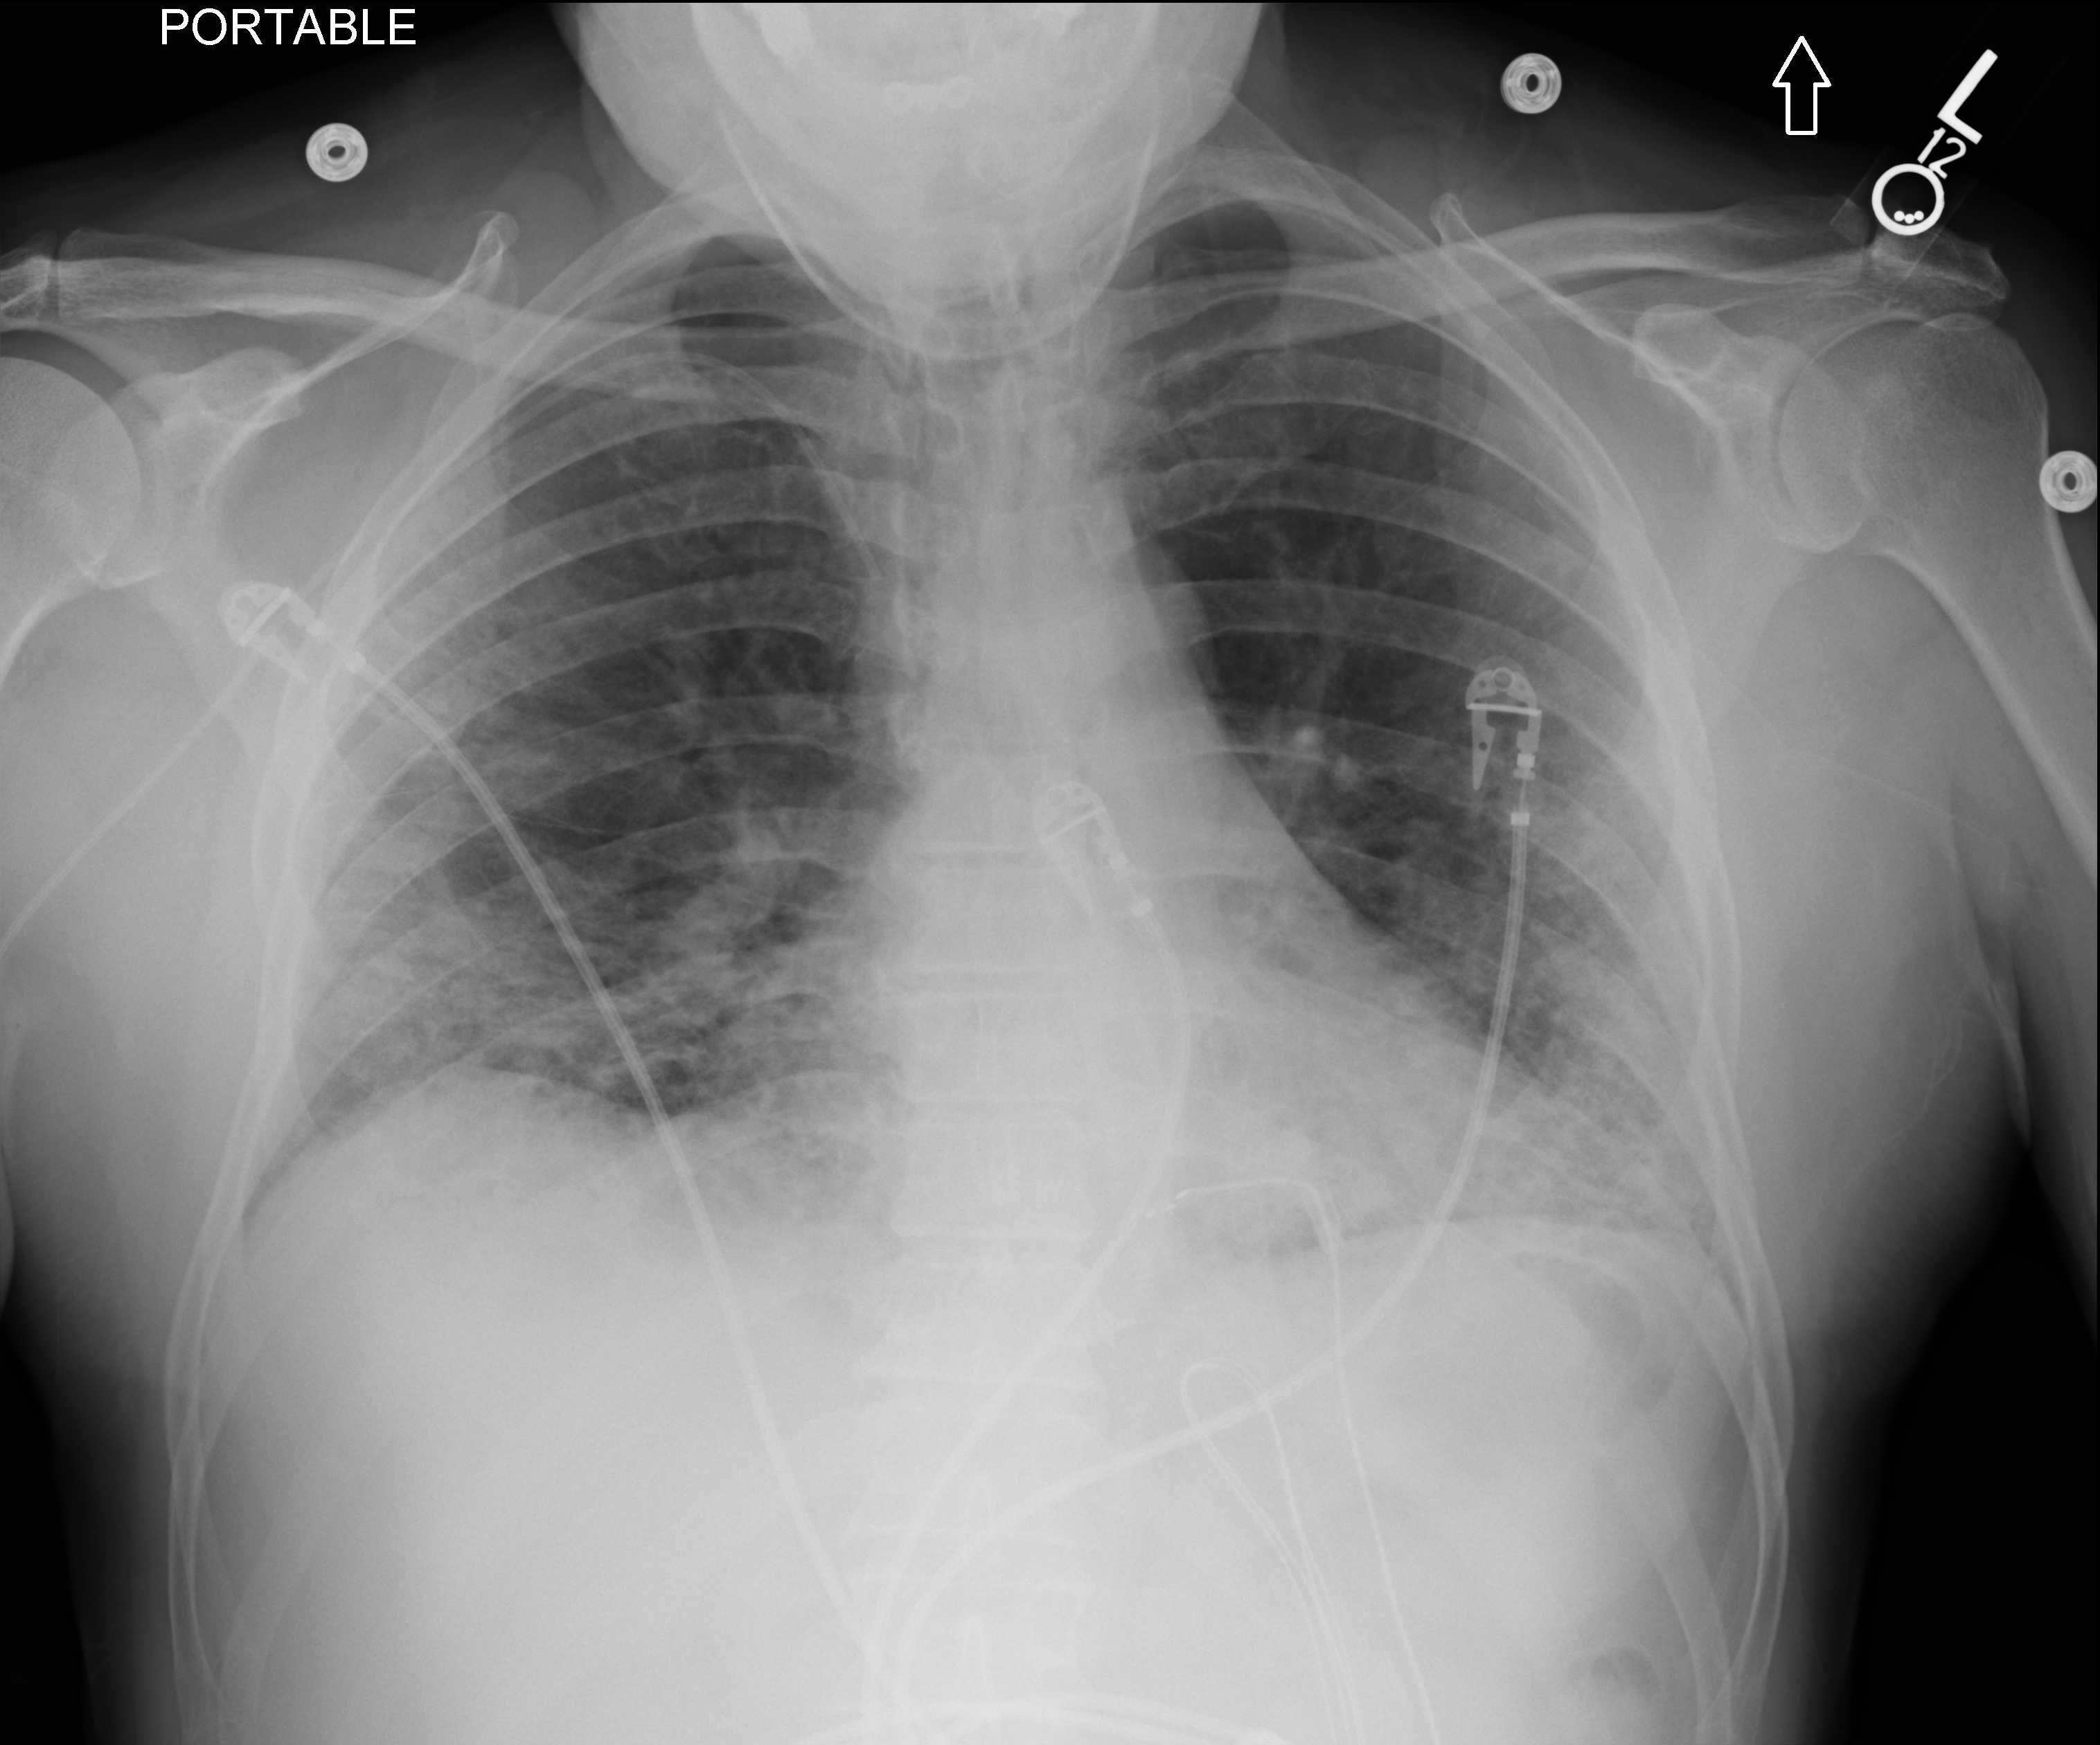
Portable chest radiograph; anteroposterior (AP) projection. Male patient hospitalised with COVID-19, age 18–59 years.
Hospital-stay facts (about this admission, not read from this image; timing relative to this image not recorded):
- length of hospital stay: 38 days
- mechanically ventilated during this hospital stay: no